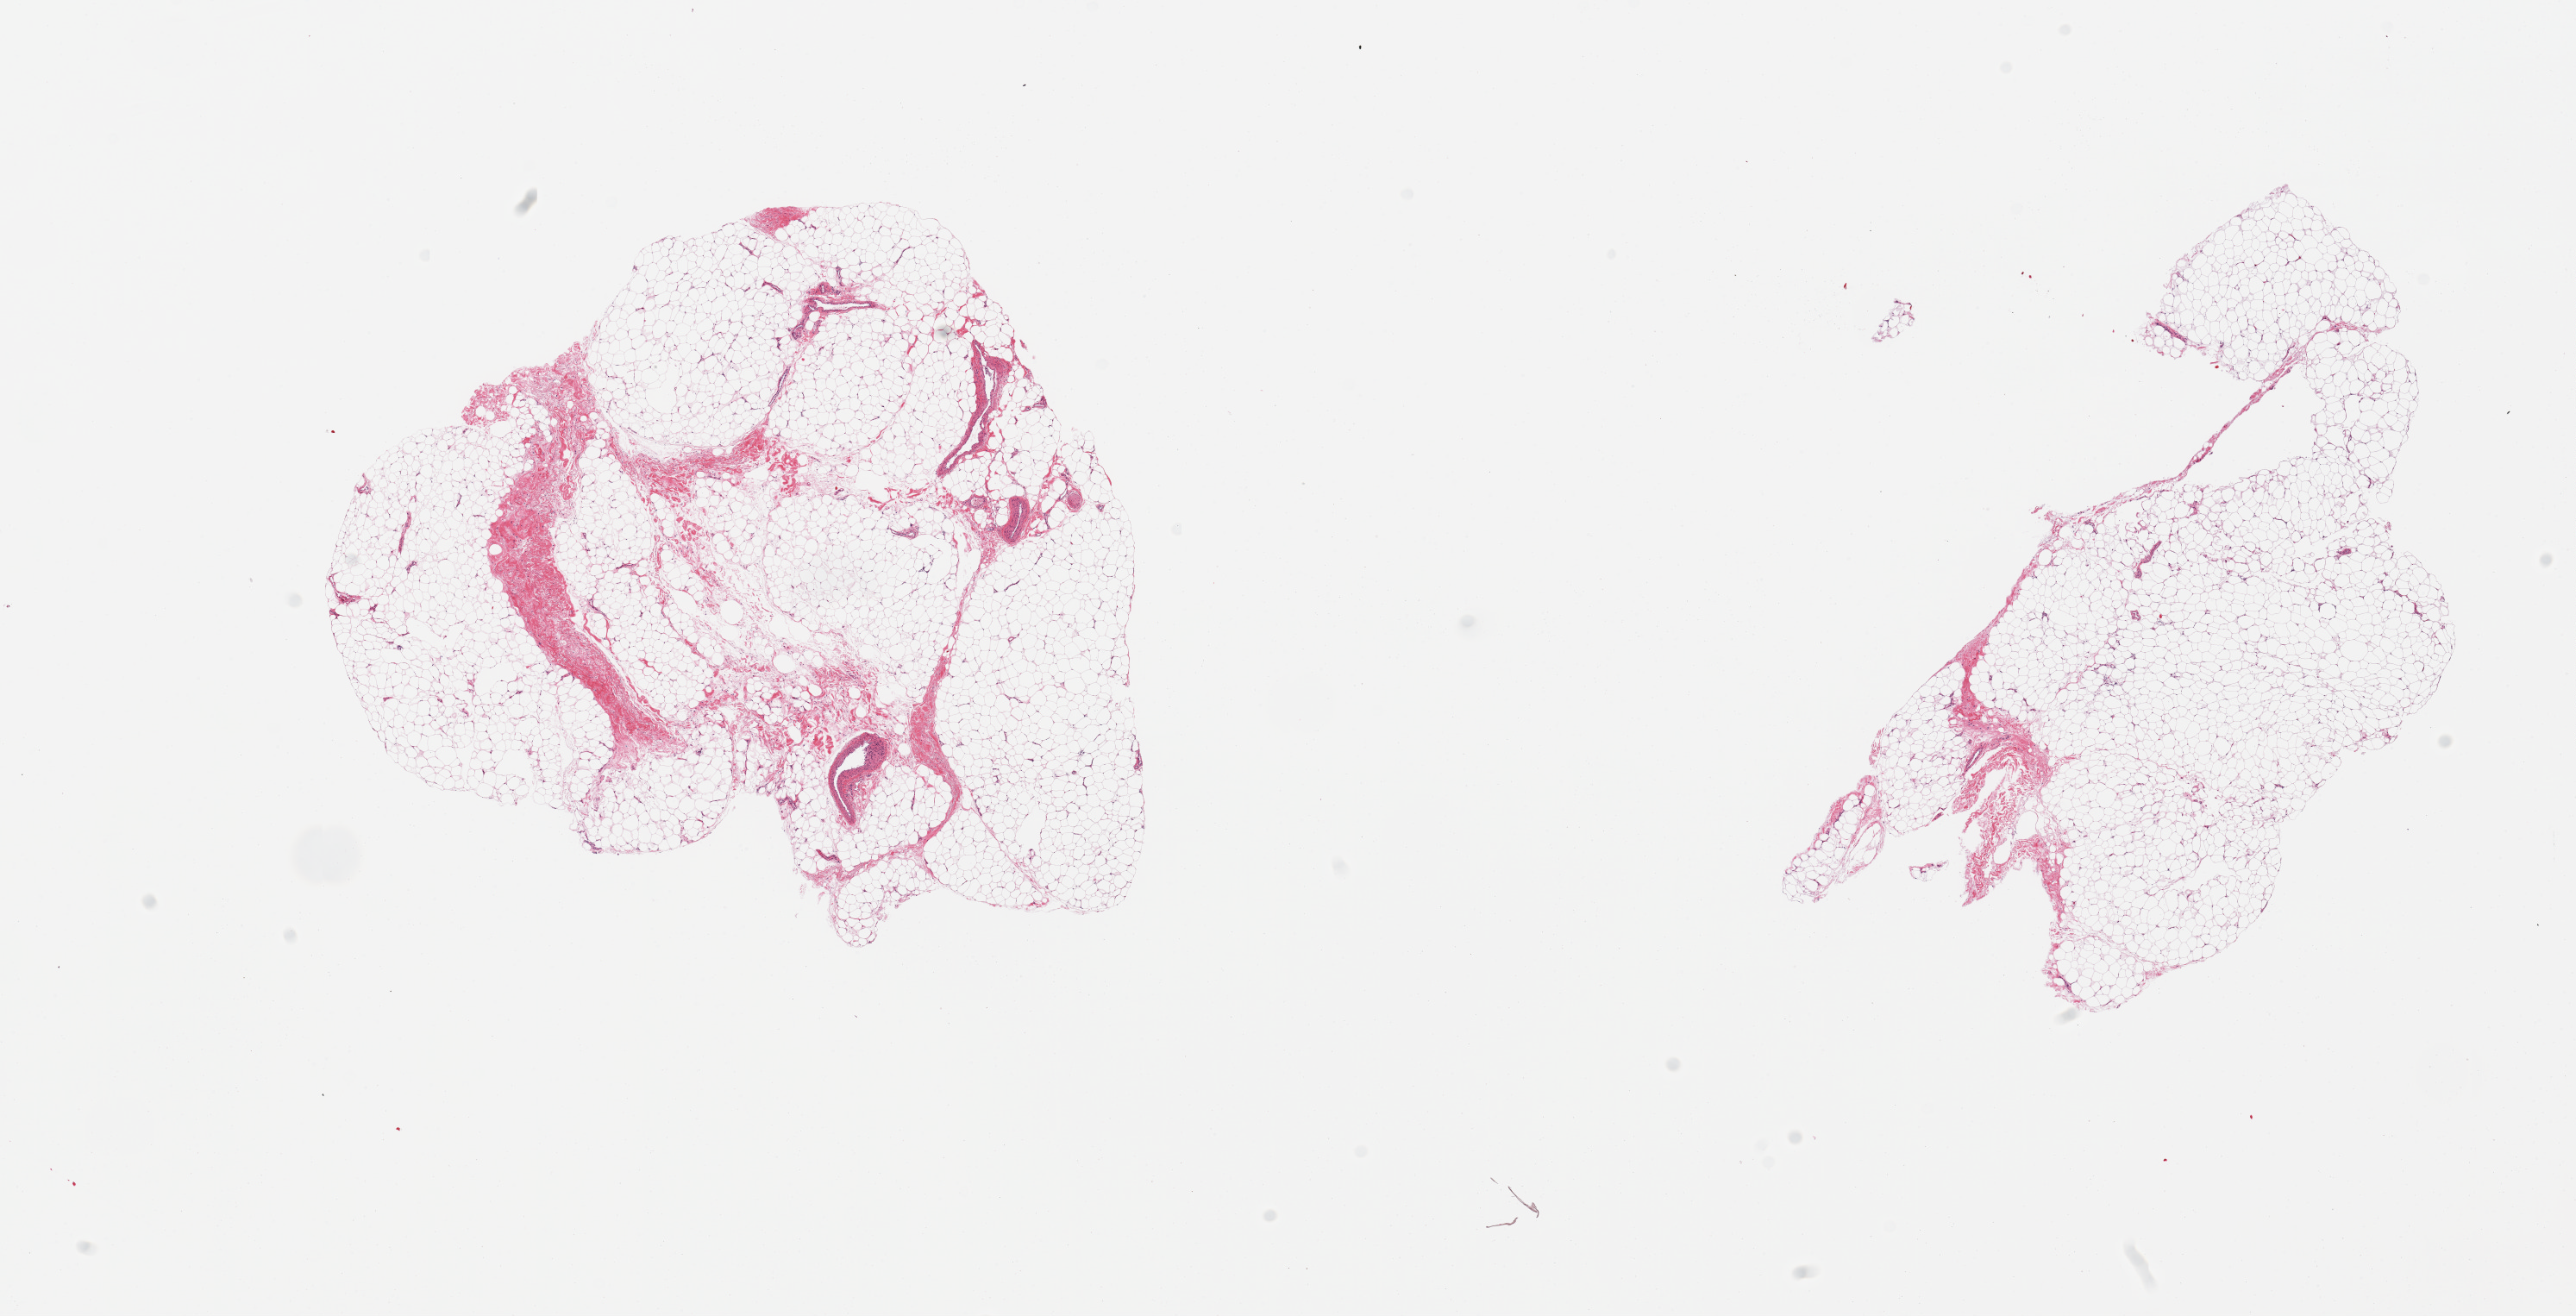
H&E whole-slide image — whole scanned area (about 23.6 x 12.1 mm, acquisition: 20x scan) shown as a low-resolution overview. PAXgene-fixed, paraffin-embedded tissue. Target tissue: adipose tissue. Donor tissue sample. Male donor.
• review note (as recorded): 2 pieces; 5-10% fibrovascular tissue